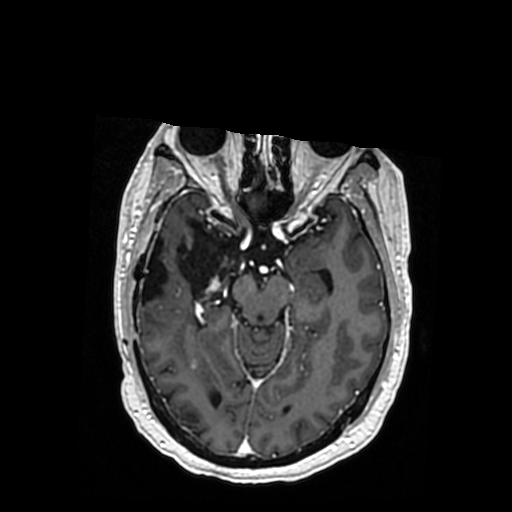
Brain MRI from a brain-tumour surgery series, one axial slice; slice 215 of 364 in the series (ordered by position); T1-weighted post-contrast; 512 × 512 image matrix, field of view 260 × 260 mm. From the clinical record (not read from this slice): histopathology: Oligodendroglioma; WHO grade: 3; IDH mutation: yes; tumour location: Right Posterior Temporal Inferior Parietal.
Annotated regions visible in this slice (manually delineated by an expert):
- previous resection cavity: bounding box [x1, y1, x2, y2] px = [140, 225, 239, 303]